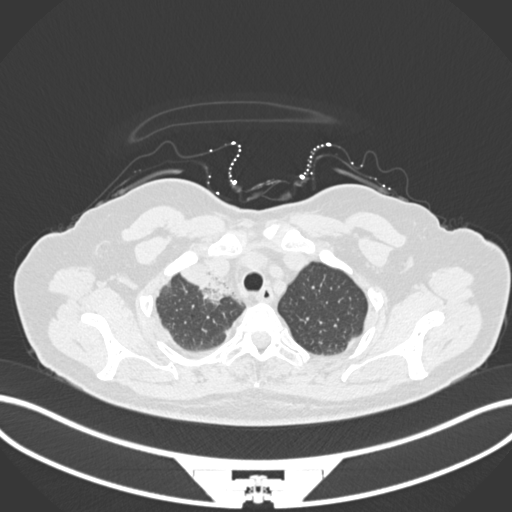
Chest CT, one axial slice; position 145 of 172 along the scan axis; 120 kVp; lung window (W 1500 / L -600 HU); 1 mm slice thickness; 512 × 512 image matrix, field of view 400 × 400 mm. Patient: female, 52 years. Case-level facts recorded for this patient, not image findings: clinical TNM (as recorded): T3 N1 M1.
Structures marked on this image (bounding box drawn by a radiologist):
- lung tumour (recorded histology: adenocarcinoma): bounding box [x1, y1, x2, y2] px = [176, 261, 233, 307]